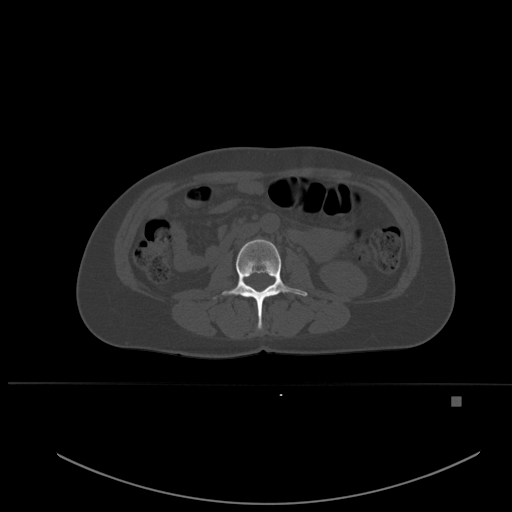
CT including the spine, one axial slice; slice 212 of 651 in the series (ordered by position); bone window (W 1800 / L 400 HU); 512 × 512 image matrix, field of view 443 × 443 mm. Patient: female, 49 years. From the clinical record (not read from this slice): primary cancer: breast.
Annotated regions visible in this slice (semi-automatically segmented with operator editing):
- L2 vertebra: box from (x=213, y=239) to (x=308, y=329) px